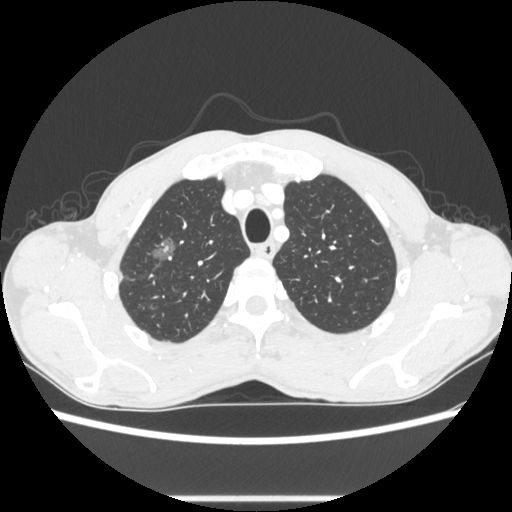
Chest CT, one axial slice. Position 235 of 289 along the scan axis. 100 kVp. Lung window (W 1500 / L -600 HU). 1.25 mm slice thickness. 512 × 512 image matrix. Patient: male, 54 years. From the clinical record (not read from this slice): clinical TNM (as recorded): T1a N0 M0.
Outlined on this slice (rectangle marked by the reading radiologist):
- lung tumour (recorded histology: adenocarcinoma): box from (x=144, y=233) to (x=176, y=267) px